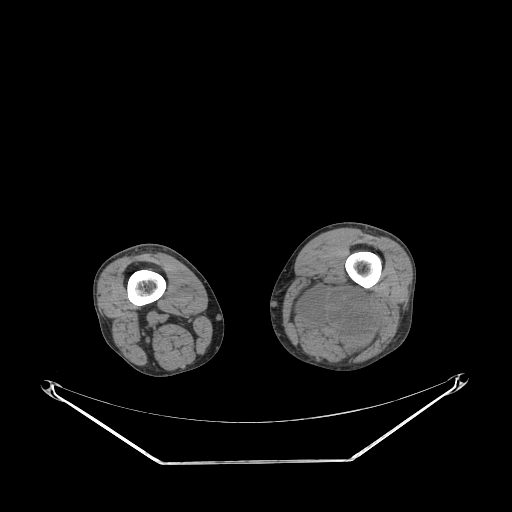
CT of an extremity soft-tissue mass (from a PET/CT study), one axial slice. Position 208 of 267 along the scan axis. Reconstruction kernel STANDARD. 140 kVp. Soft-tissue window (W 400 / L 40 HU). 3.75 mm slice thickness. 512 × 512 image matrix, field of view 500 × 500 mm. Male patient. From the clinical record (not read from this slice): histological type: undifferentiated pleomorphic liposarcoma; grade: high; site of the primary tumour: left thigh.
Structures marked on this image (expert contour drawn on MRI and transferred to this co-registered scan by the dataset authors):
- gross tumour volume including surrounding oedema: bounding box (x1, y1, x2, y2) in pixels: (290, 276, 378, 357)
- gross tumour volume (mass): (301, 292, 366, 339)